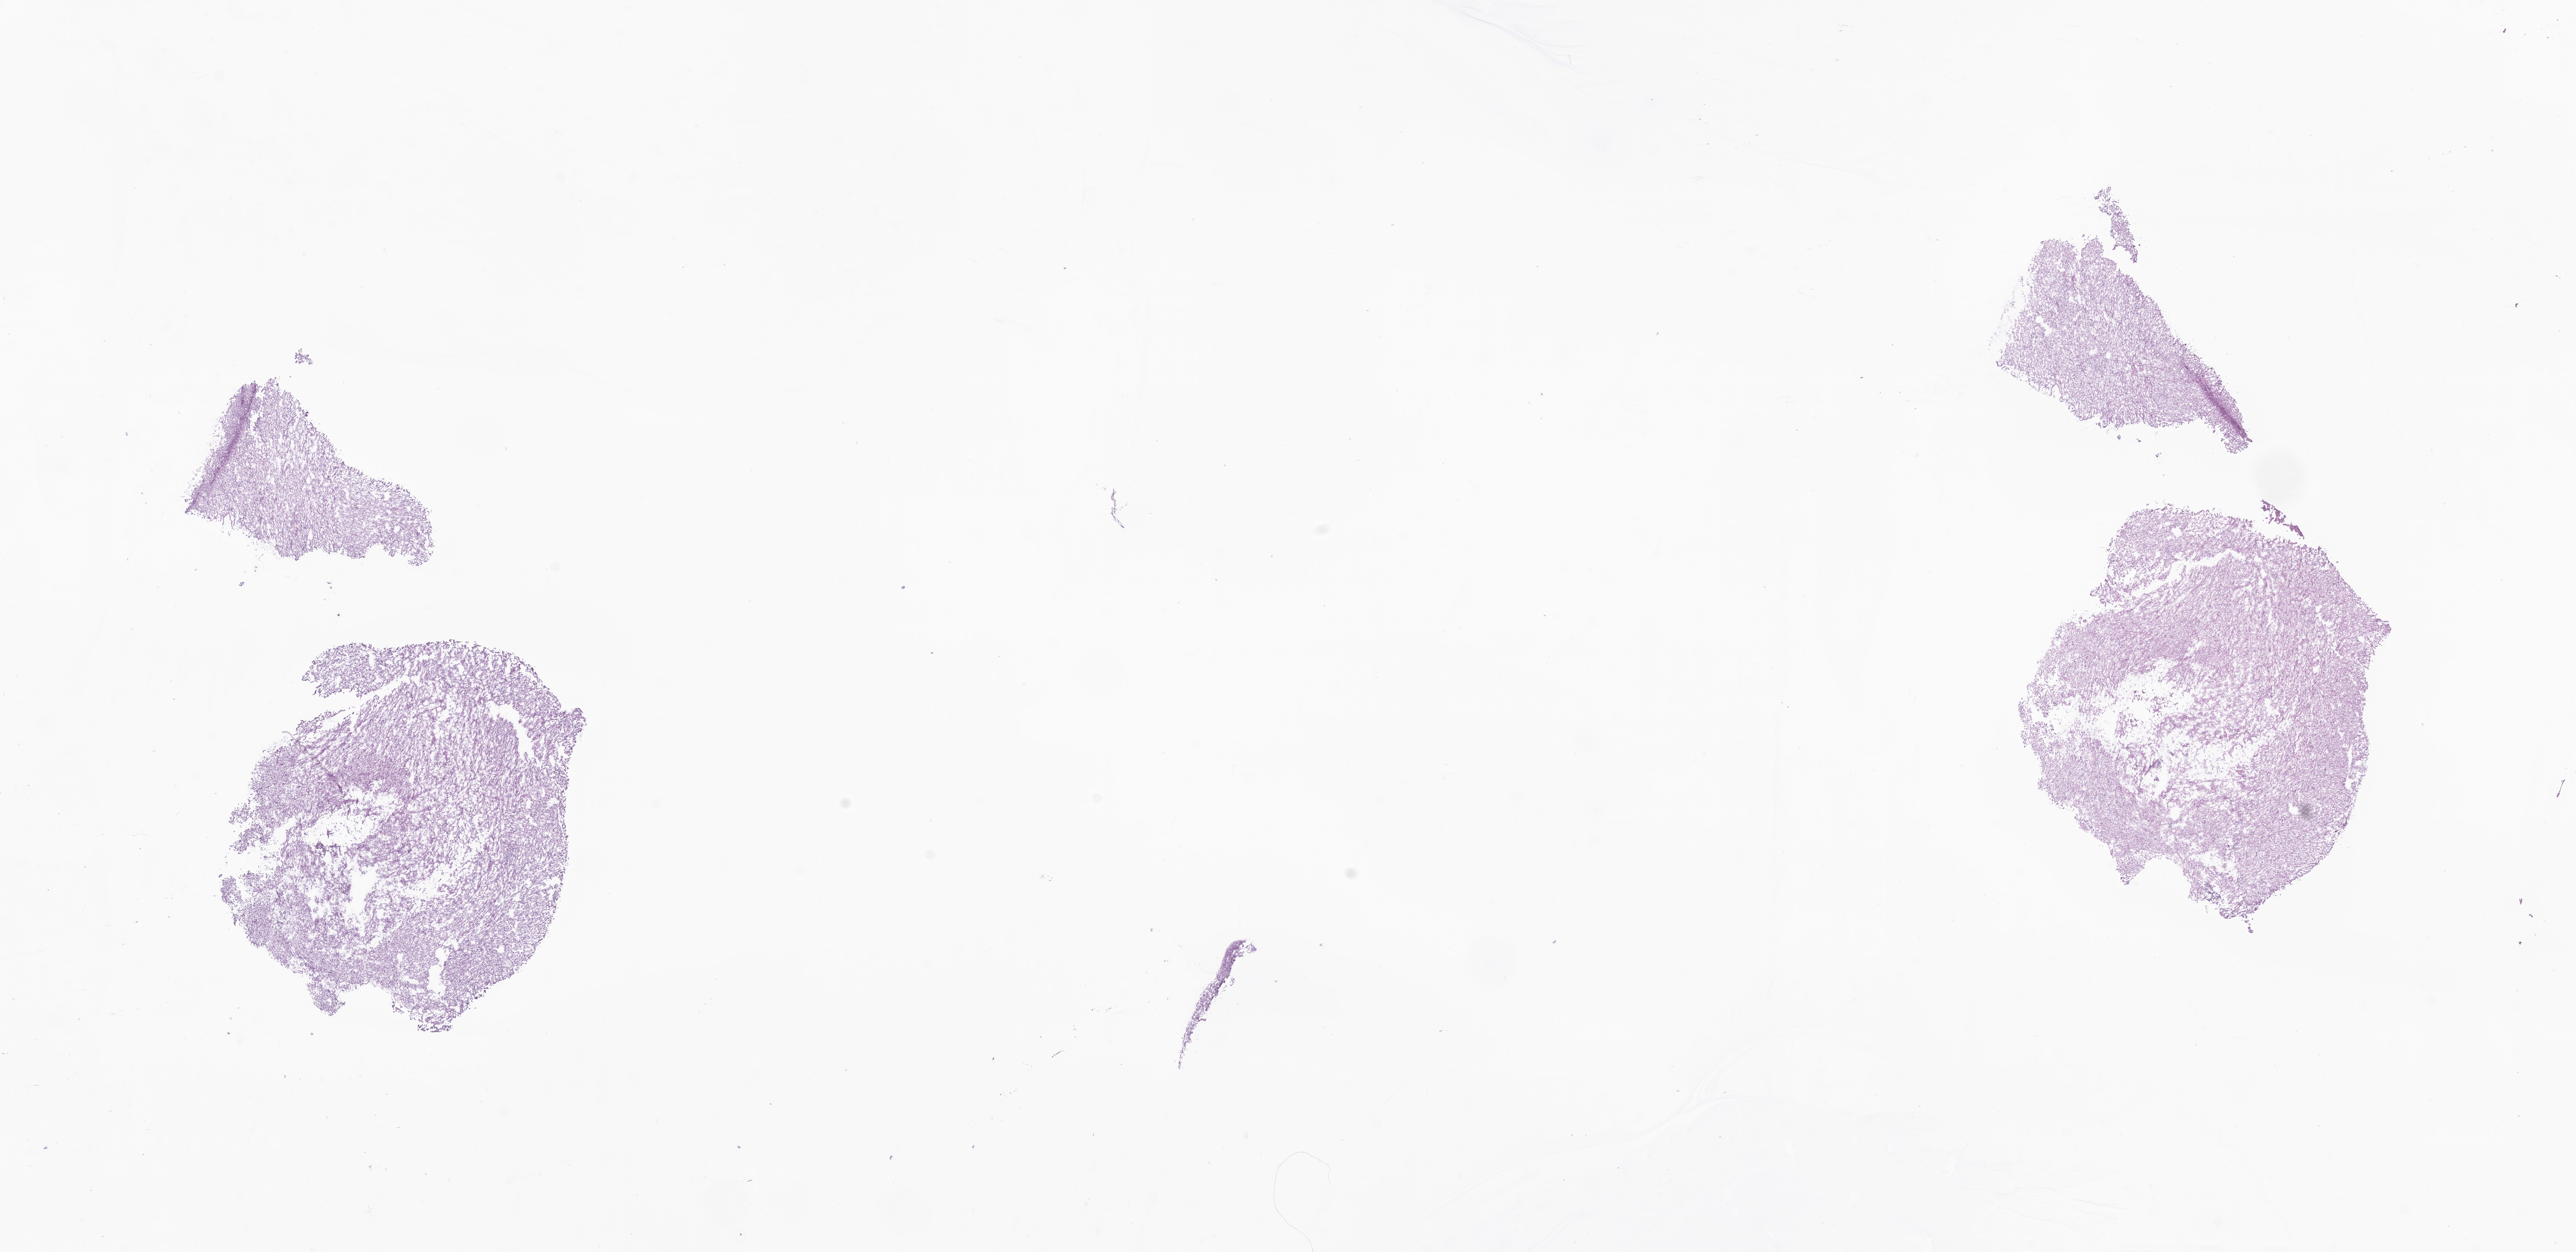
Digitized haematoxylin and eosin-stained section of tumor tissue from the brain — low-resolution overview of the scanned area, about 25.4 x 12.3 mm. Frozen section. Patient male; age 124 months (10 years 4 months).
* diagnosis: Ganglioglioma, NOS